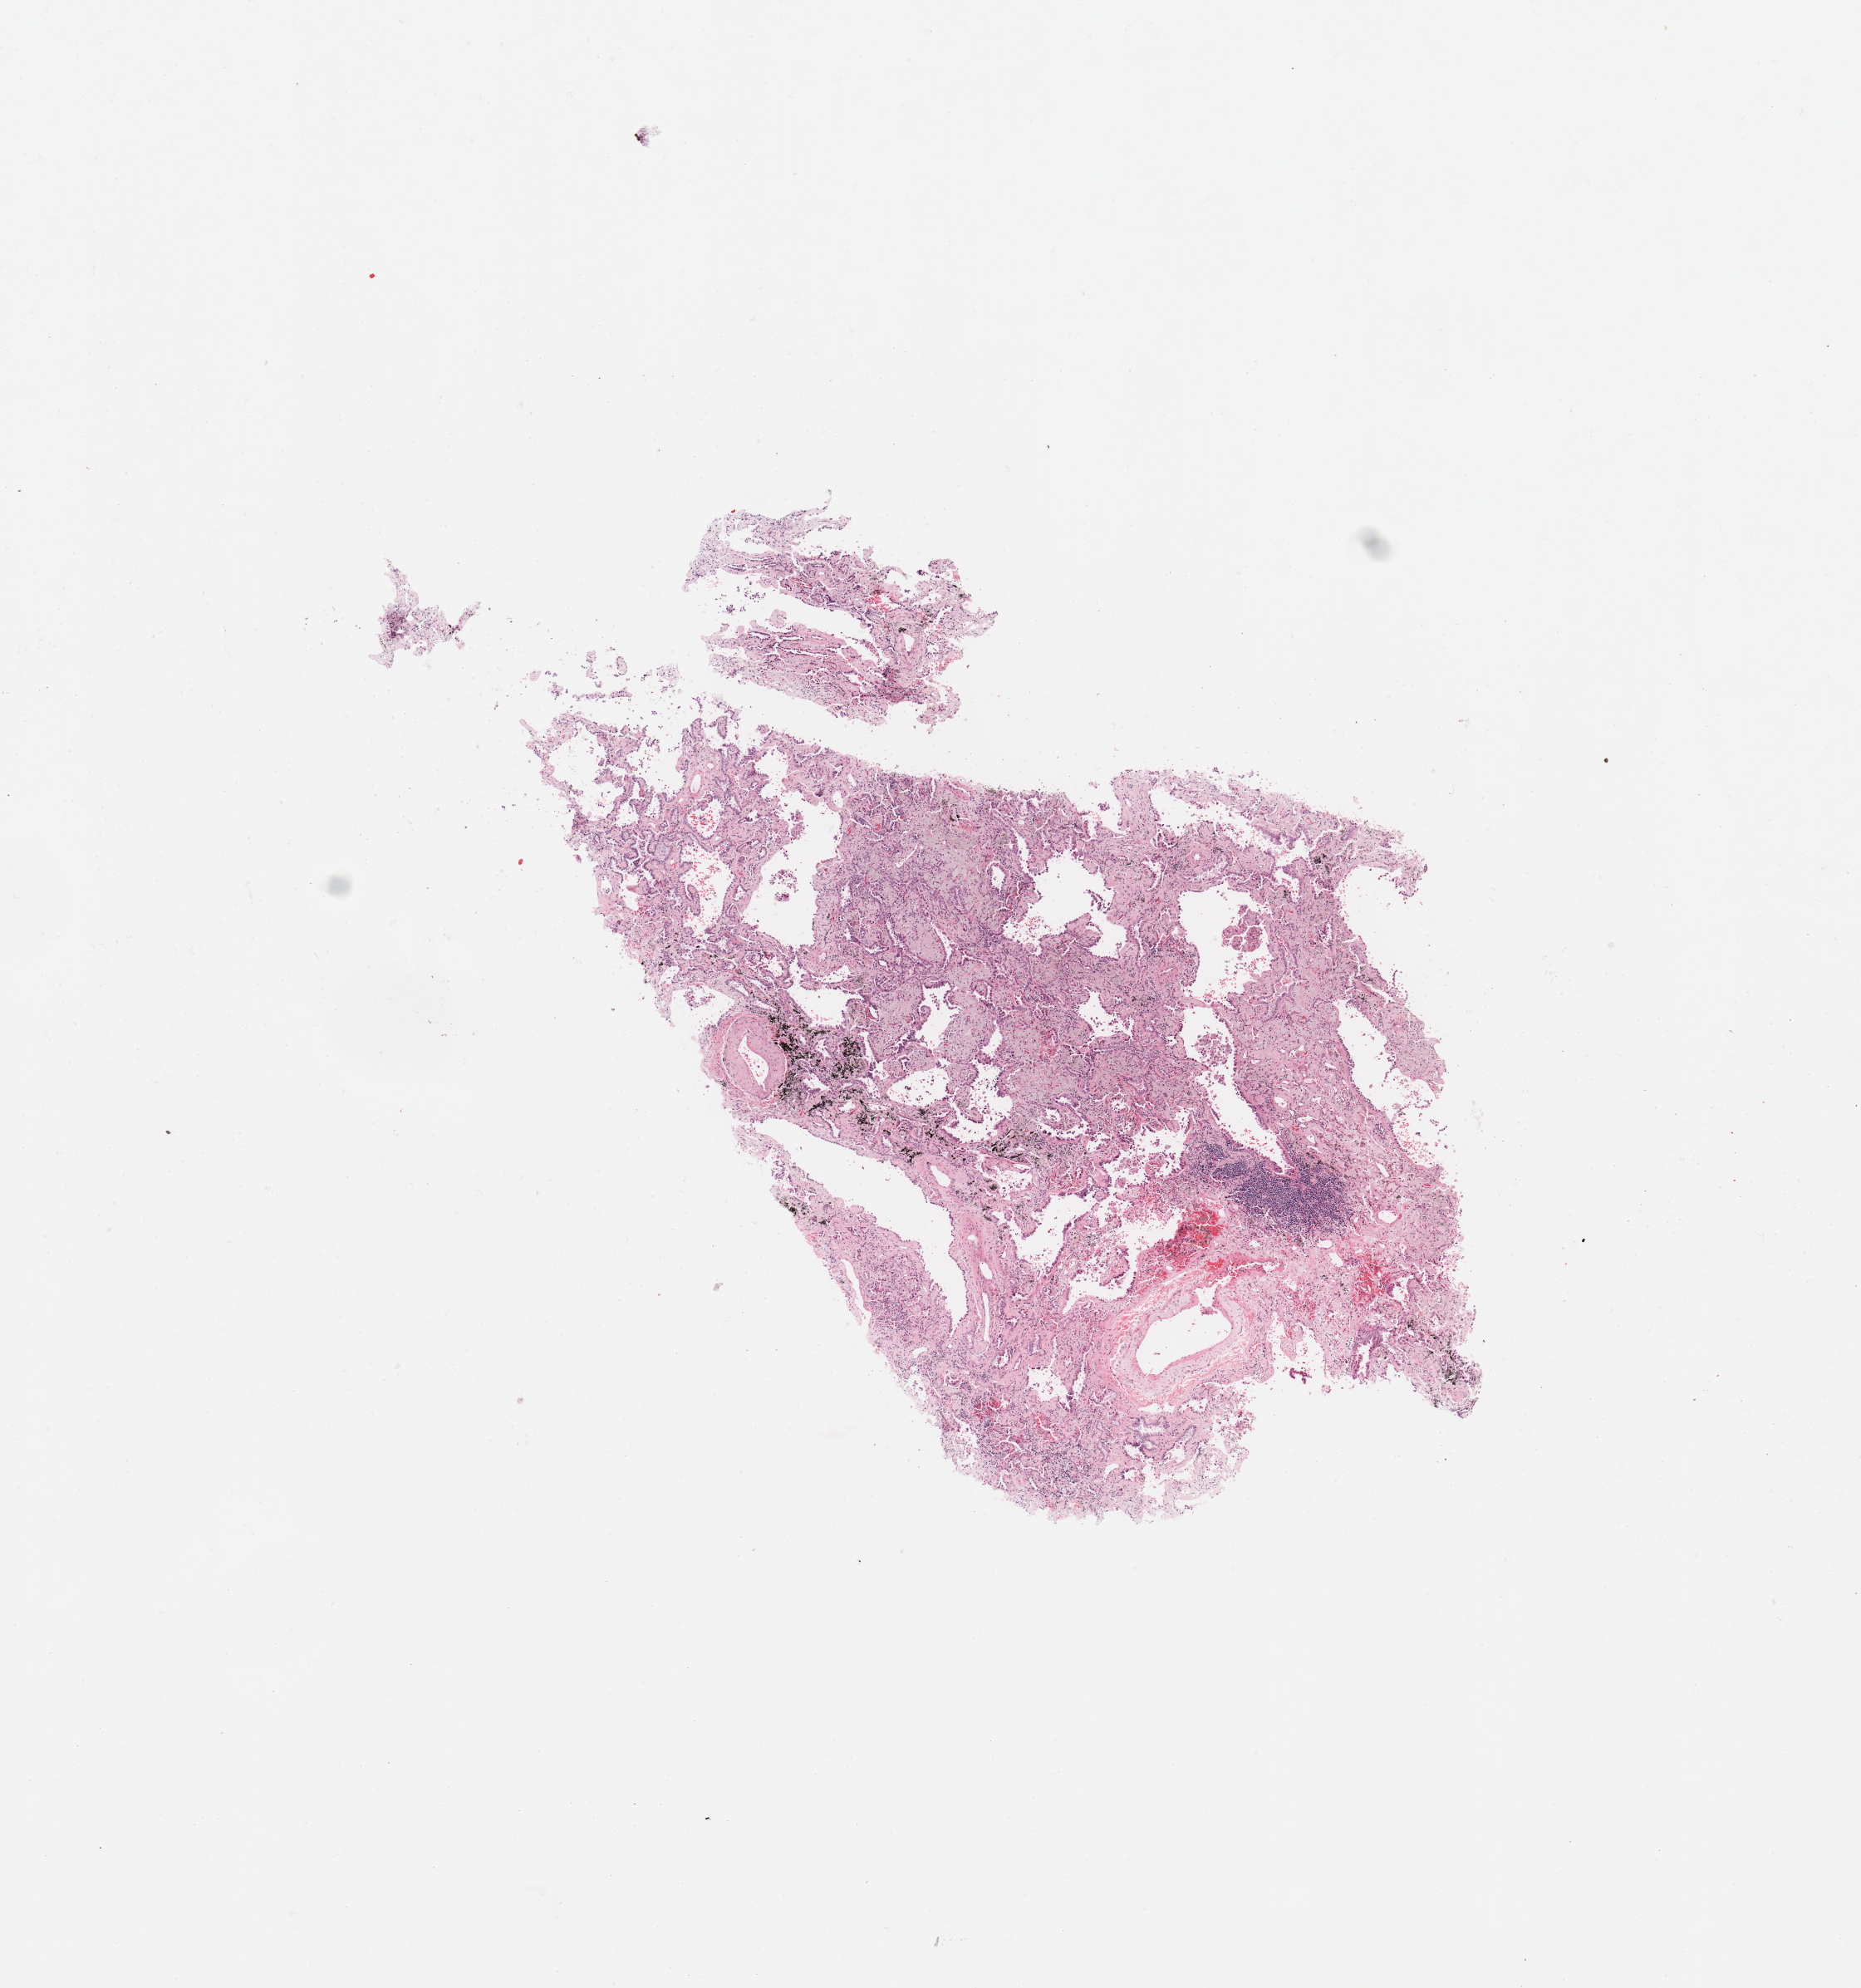
Digitized H&E-stained tissue section (whole slide) — low-resolution overview of the scanned area, about 8.9 x 9.5 mm (slide scanned at 20x), tumour tissue sample, sampled site: lung. 58-year-old male patient. Histologic grade: G2 (moderately differentiated). Composition of this section per pathologist review: tumour nuclei 50%, necrosis 0%.
Primary tumour site (as recorded): left upper lobe. Diagnosis: Adenocarcinoma, NOS. AJCC pathologic stage: IA3.